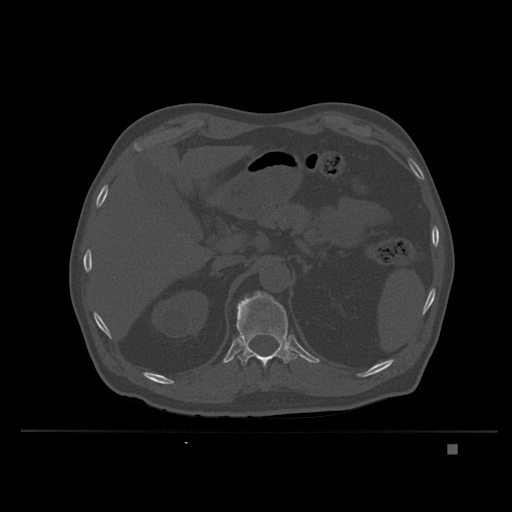
CT including the spine, one axial slice; position 160 of 435 along the scan axis; bone window (W 1800 / L 400 HU); 1.5 mm slice thickness; 512 × 512 image matrix, field of view 434 × 434 mm. Patient: male, 73 years. Case-level facts recorded for this patient, not image findings: primary cancer: skin.
Annotated regions visible in this slice (semi-automatic segmentation, software-assisted and operator-edited):
- T11 vertebra: box from (x=262, y=385) to (x=265, y=388) px
- T12 vertebra: (x=235, y=291)–(x=298, y=368)